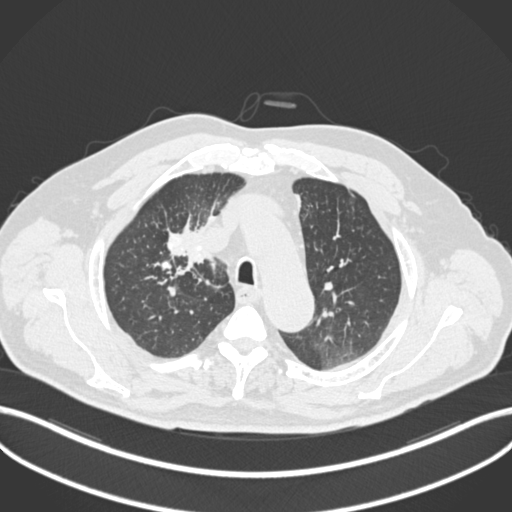
Chest CT, one axial slice. Position 153 of 255 along the scan axis. 120 kVp. Lung window (W 1500 / L -600 HU). 1 mm slice thickness. 512 × 512 image matrix, field of view 400 × 400 mm. Patient: male, 60 years. From the clinical record (not read from this slice): clinical TNM (as recorded): T1b N1 M0.
Structures marked on this image (rectangle marked by the reading radiologist):
- lung tumour (recorded histology: squamous cell carcinoma): bounding box [x1, y1, x2, y2] px = [167, 221, 215, 278]